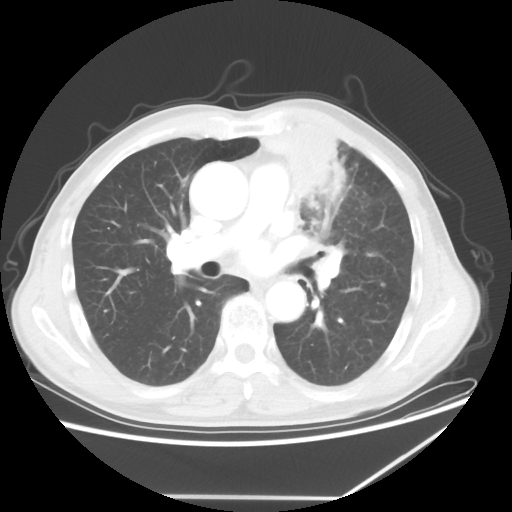
Chest CT, one axial slice; reconstruction kernel STANDARD; 100 kVp; lung window (W 1500 / L -600 HU); 5 mm slice thickness; 512 × 512 image matrix, field of view 383 × 383 mm. Patient: male, 64 years. Case-level facts recorded for this patient, not image findings: clinical TNM (as recorded): T1c N1 M1; histopathological grade: G2.
Structures marked on this image (rectangle marked by the reading radiologist):
- lung tumour (recorded histology: squamous cell carcinoma): bounding box <256,123,366,225> (left, top, right, bottom; pixels)